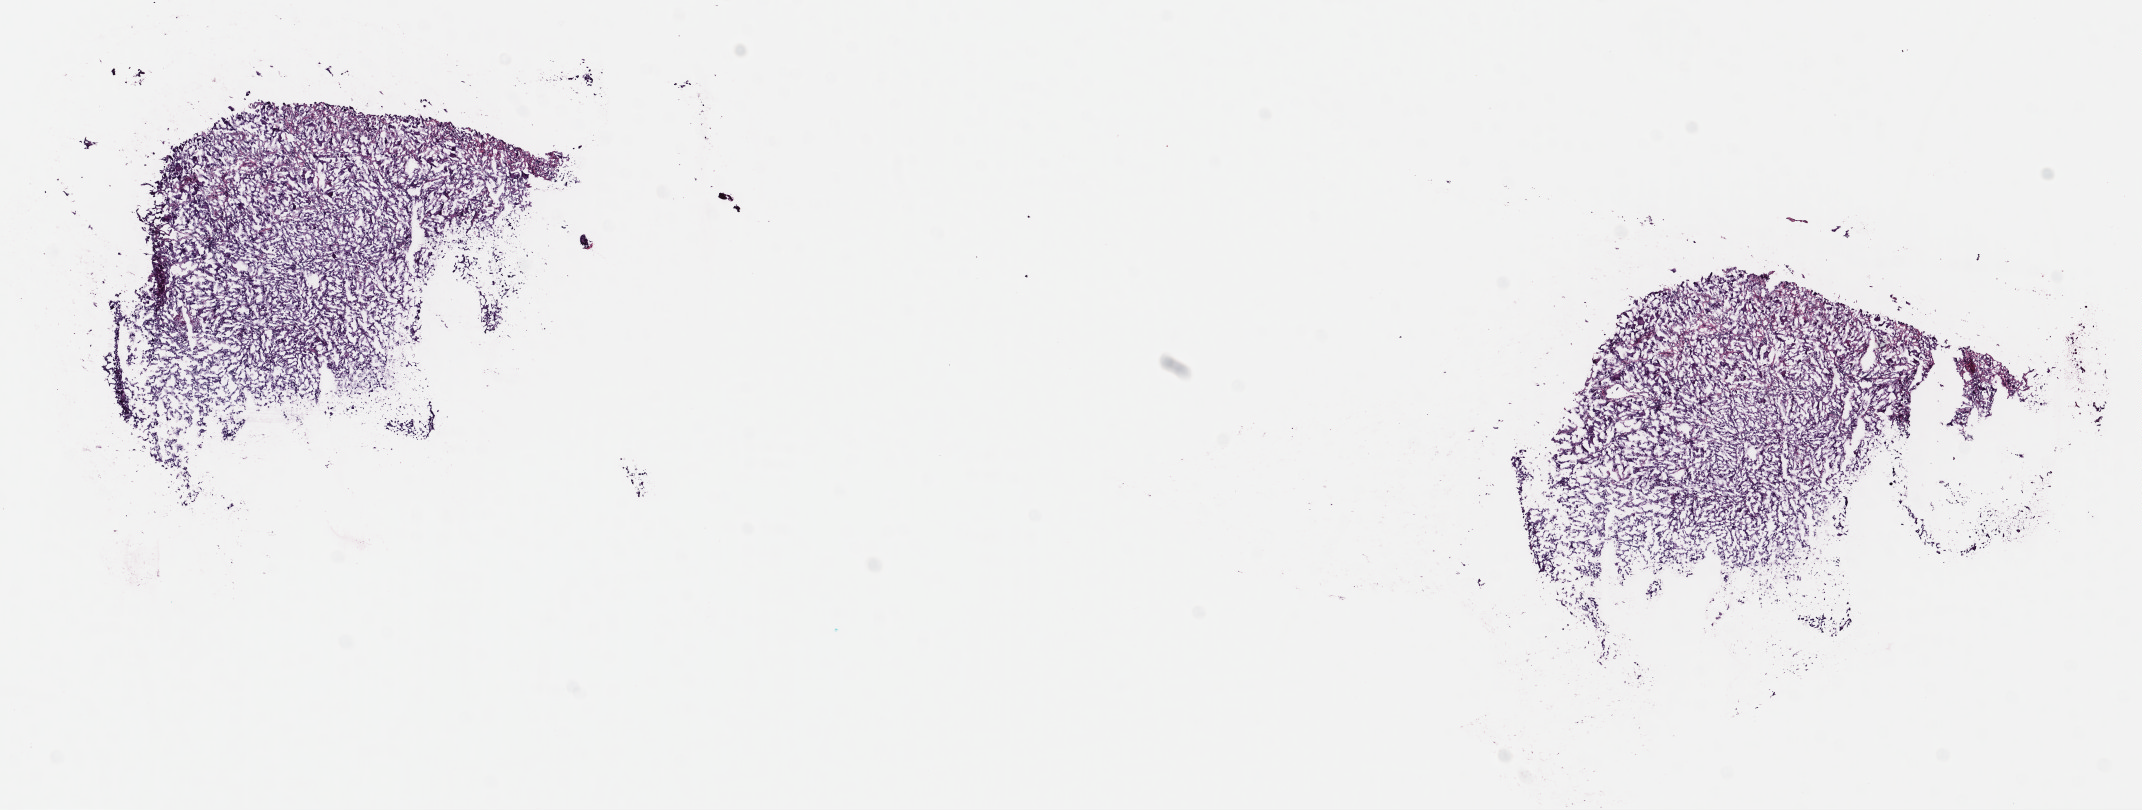
Whole-slide histology image, Hematoxylin and eosin (H&E) stained, whole scanned area (about 16.8 x 6.4 mm) shown as a low-resolution overview; frozen section from the top of the tissue portion; metastatic tumour sample, sampled site not recorded. Patient: male, age at initial diagnosis 66 years. Slide review estimates, as recorded: tumour cells 100%, tumour nuclei 80%, normal cells 0%, stromal cells 0%, necrosis 0%. Inflammatory infiltration, as recorded: lymphocyte infiltration 0%, monocyte infiltration 0%, neutrophil infiltration 0%.
This section: metastatic tumour tissue. Patient diagnosis: Malignant melanoma, NOS.